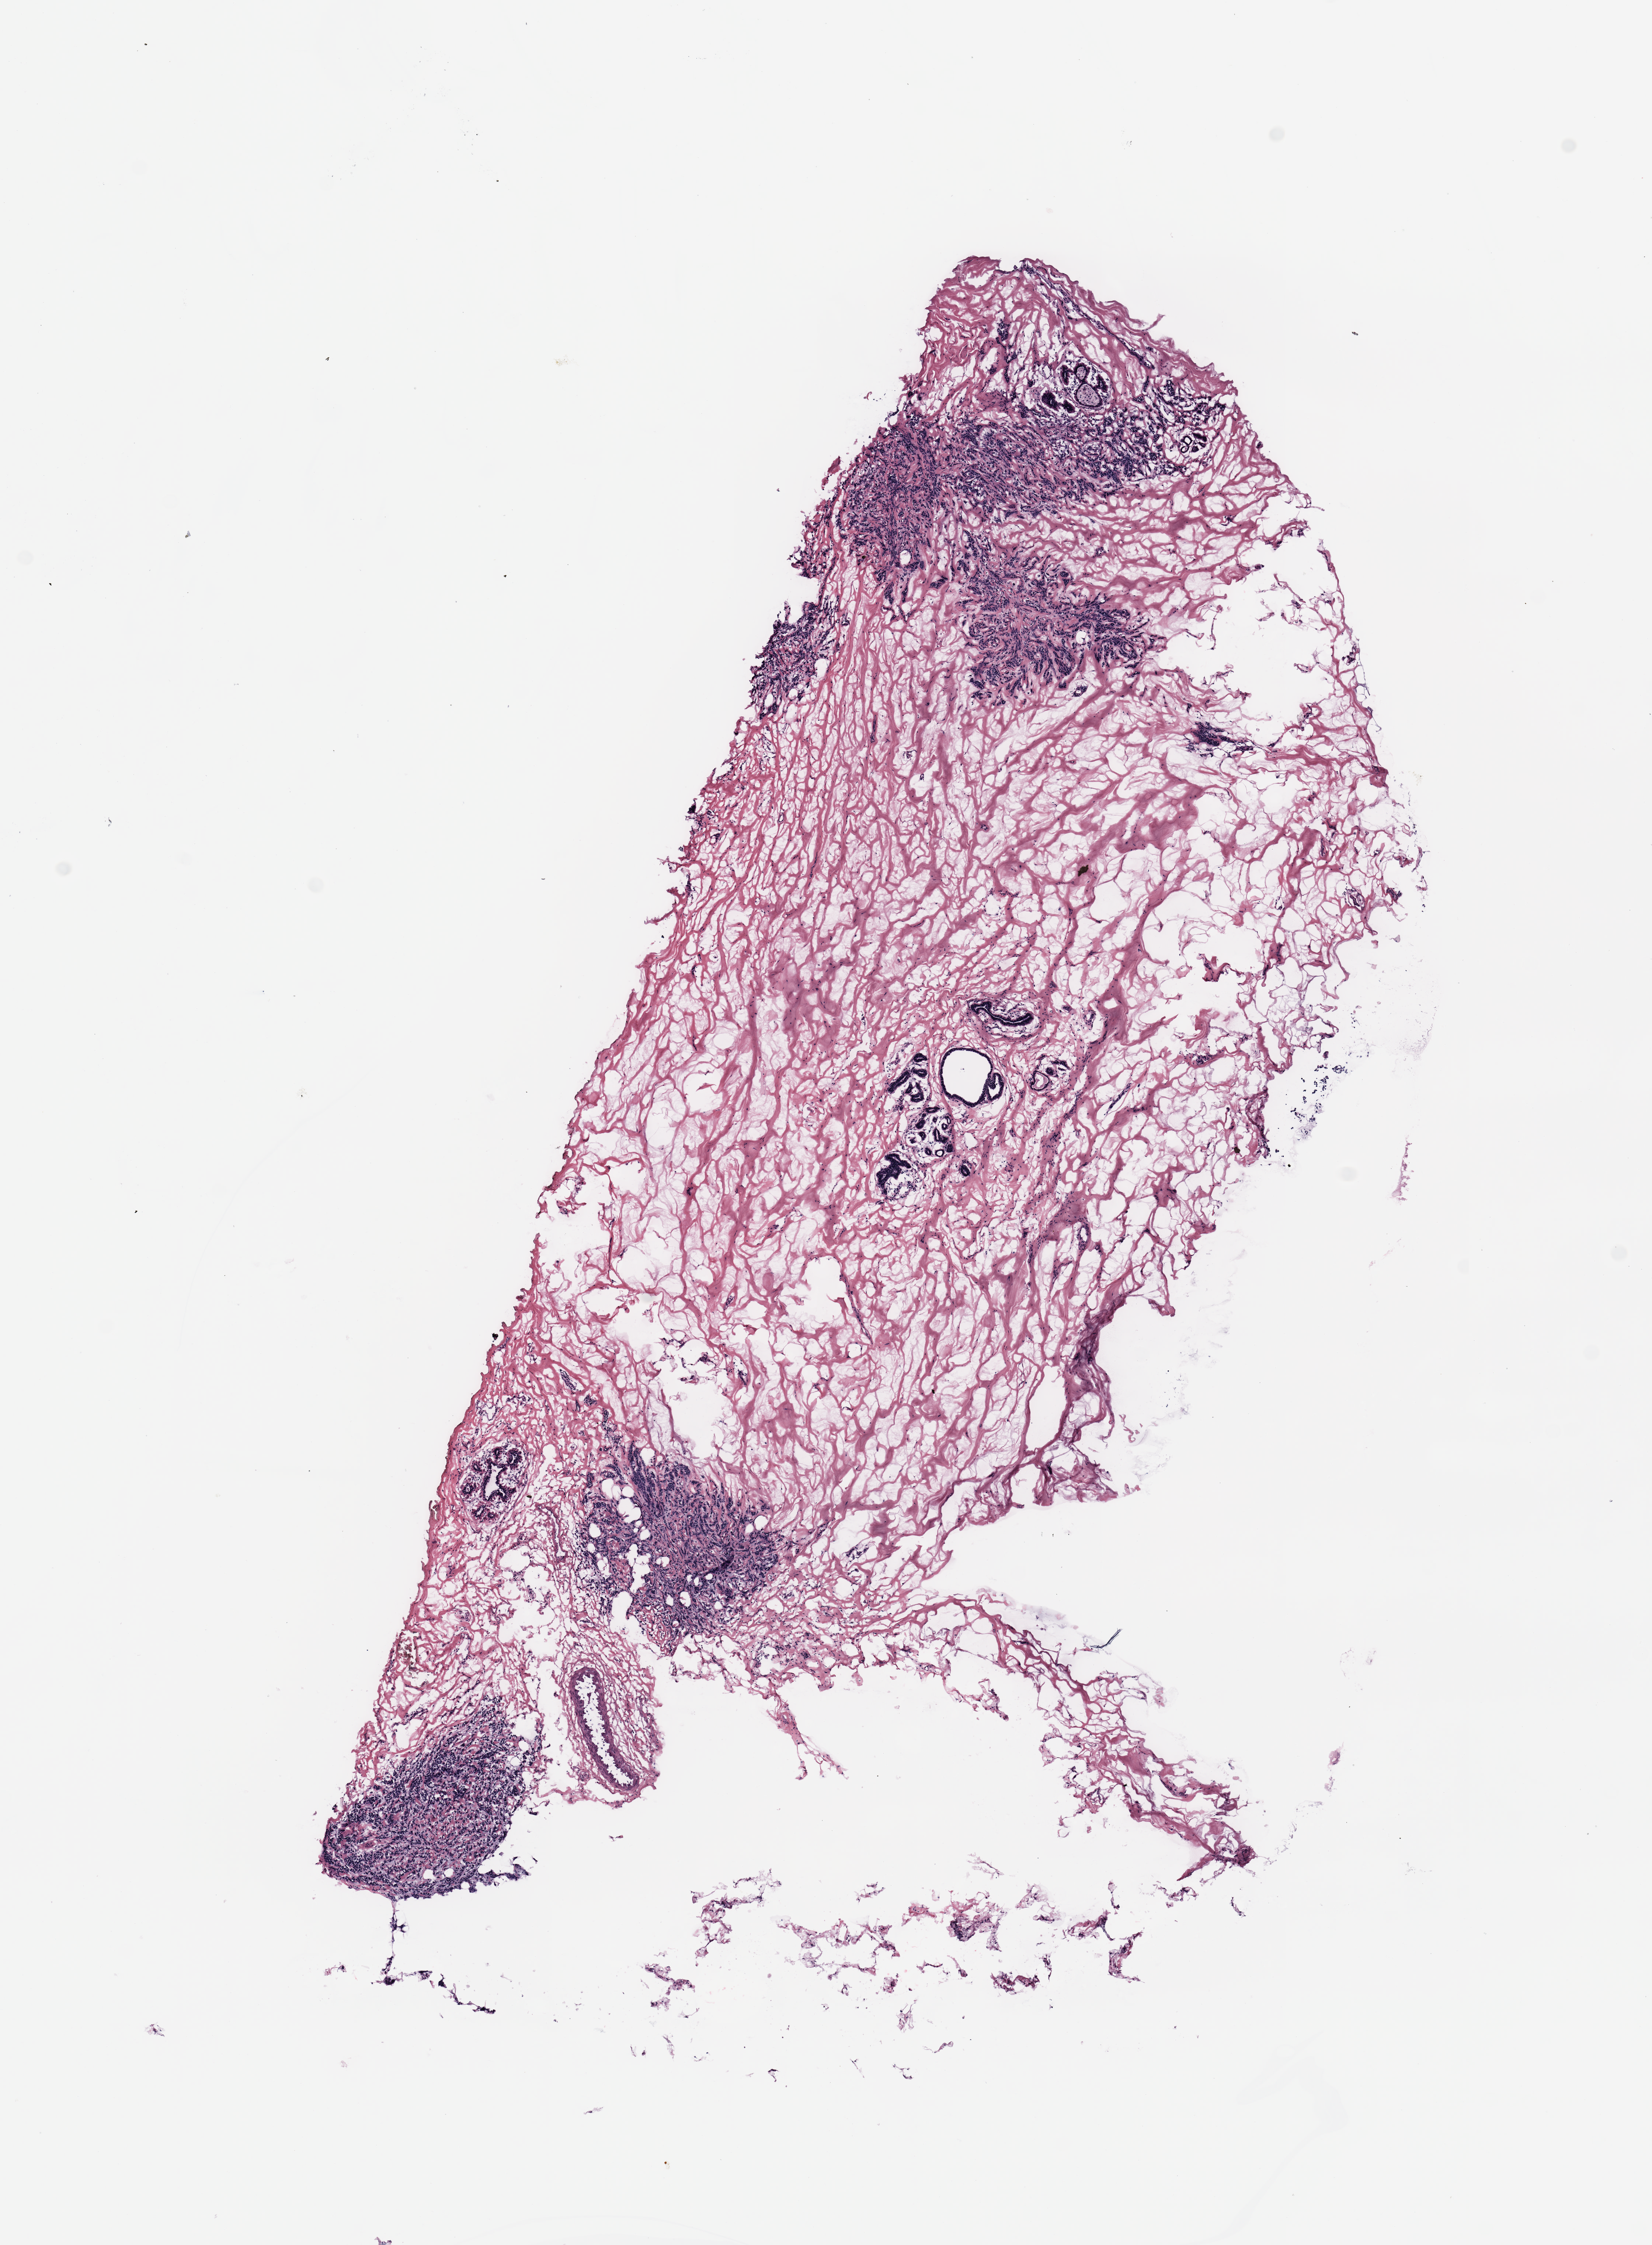
H&E whole-slide image, whole scanned area (about 8.9 x 12.0 mm, slide scanned at 20x) shown as a low-resolution overview. 46-year-old female patient.
Specimen: breast, tumour tissue.